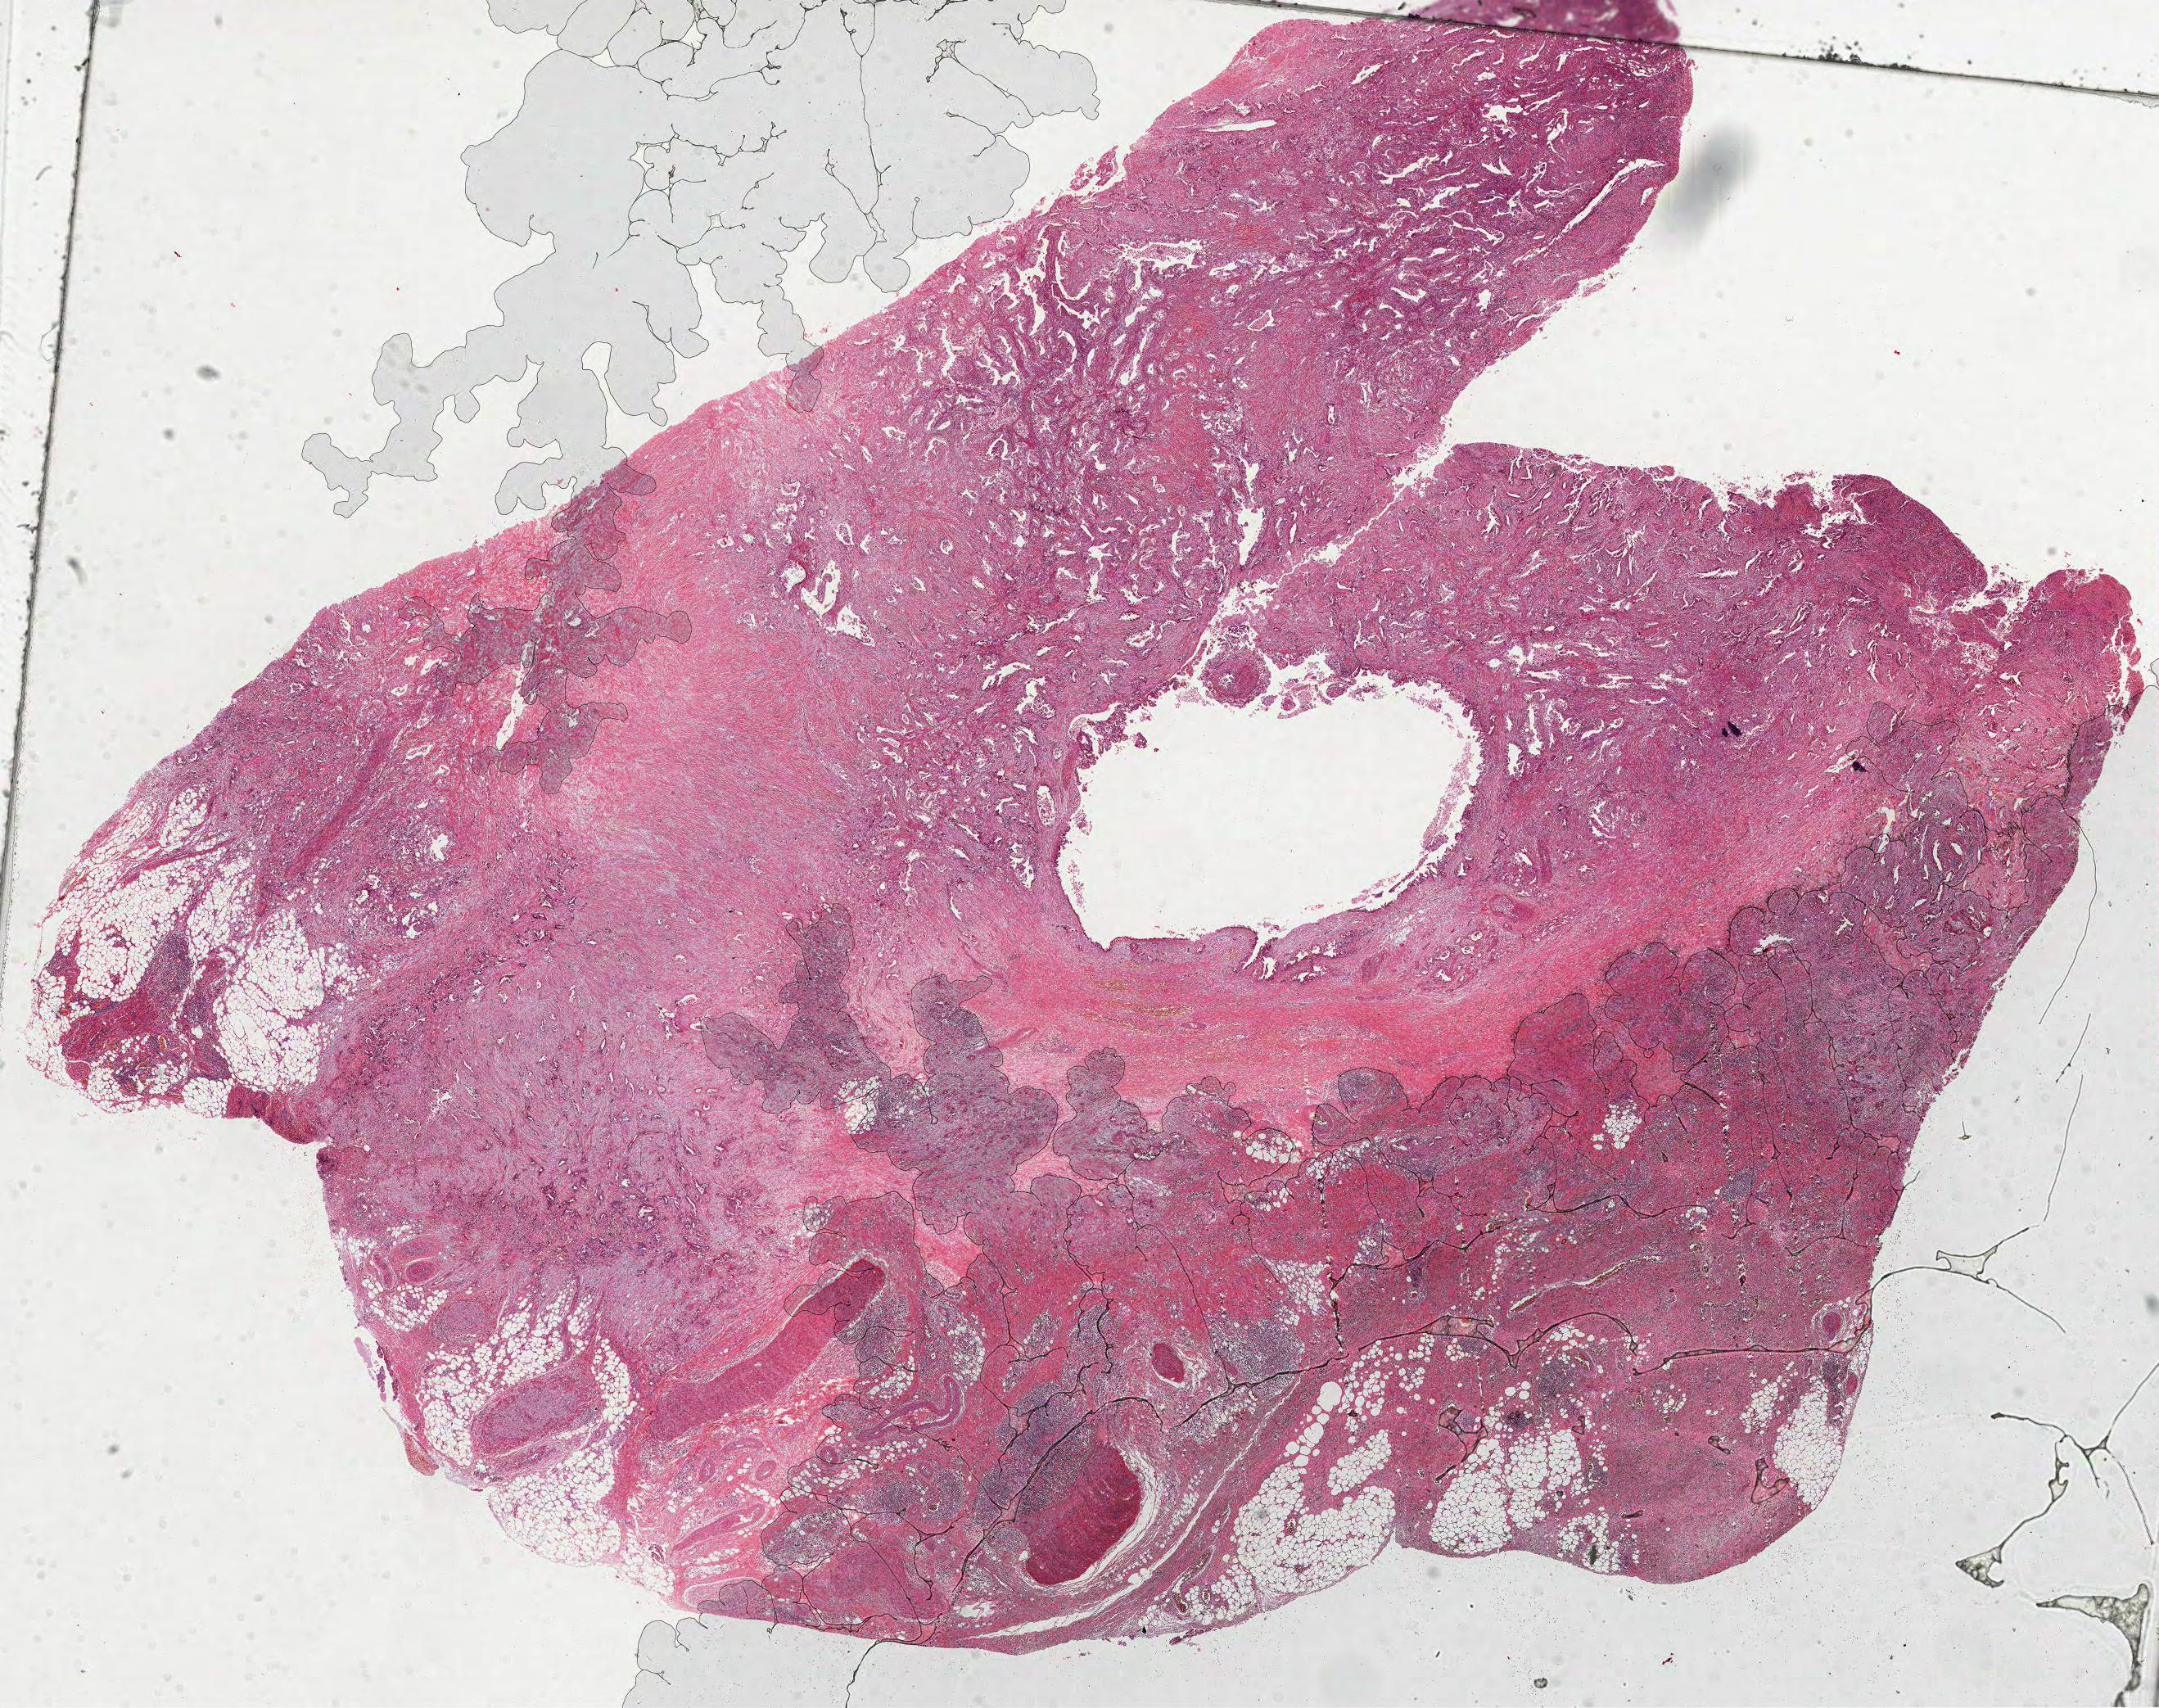
Whole-slide histology image, H&E-stained, whole scanned area (about 21.3 x 16.8 mm, acquisition: 40x scan) shown as a low-resolution overview. Formalin-fixed paraffin-embedded (FFPE) diagnostic section. Sample: primary tumour, stomach. Male patient; age at initial diagnosis 58 years. Histologic grade: G2 (moderately differentiated).
* AJCC pathologic stage: II
* diagnosis: Adenocarcinoma, NOS (cardia, NOS)